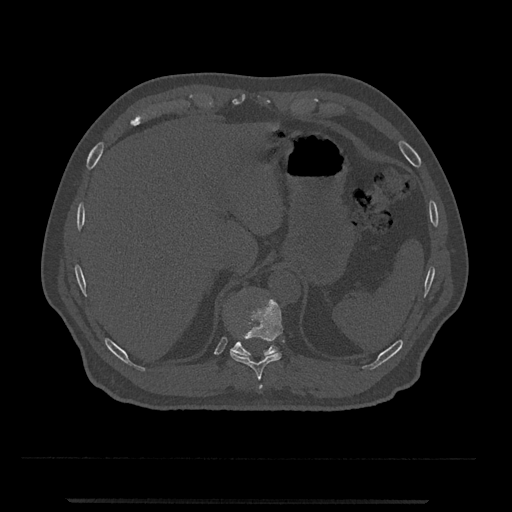
CT including the spine, one axial slice. Position 499 of 797 along the scan axis. 120 kVp. Bone window (W 1800 / L 400 HU). 0.5 mm slice thickness. 512 × 512 image matrix, field of view 419 × 419 mm. Male patient, age 63 years. From the clinical record (not read from this slice): primary cancer: prostate.
Outlined on this slice (semi-automatic segmentation, software-assisted and operator-edited):
- T10 vertebra: bounding box <230,298,283,381> (left, top, right, bottom; pixels)
- T11 vertebra: <230,341,278,356>
- T9 vertebra: <259,385,263,389>